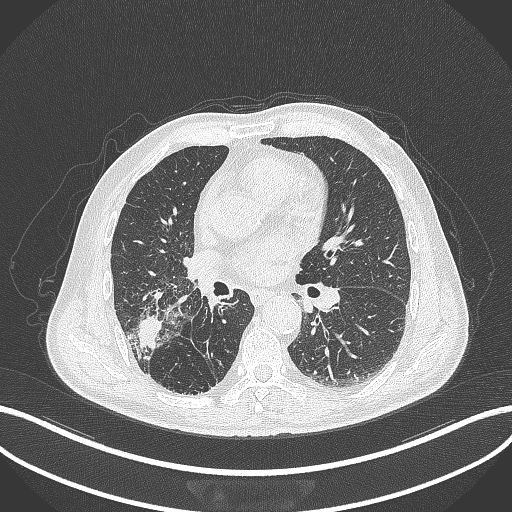
Chest CT, one axial slice; reconstruction kernel B70f; 120 kVp; lung window (W 1500 / L -600 HU); 1 mm slice thickness; 512 × 512 image matrix. Patient: male, 72 years. From the clinical record (not read from this slice): clinical TNM (as recorded): T3 N2 M0.
Structures marked on this image (bounding box drawn by a radiologist):
- lung tumour (recorded histology: adenocarcinoma): bounding box (x1, y1, x2, y2) in pixels: (131, 309, 167, 355)